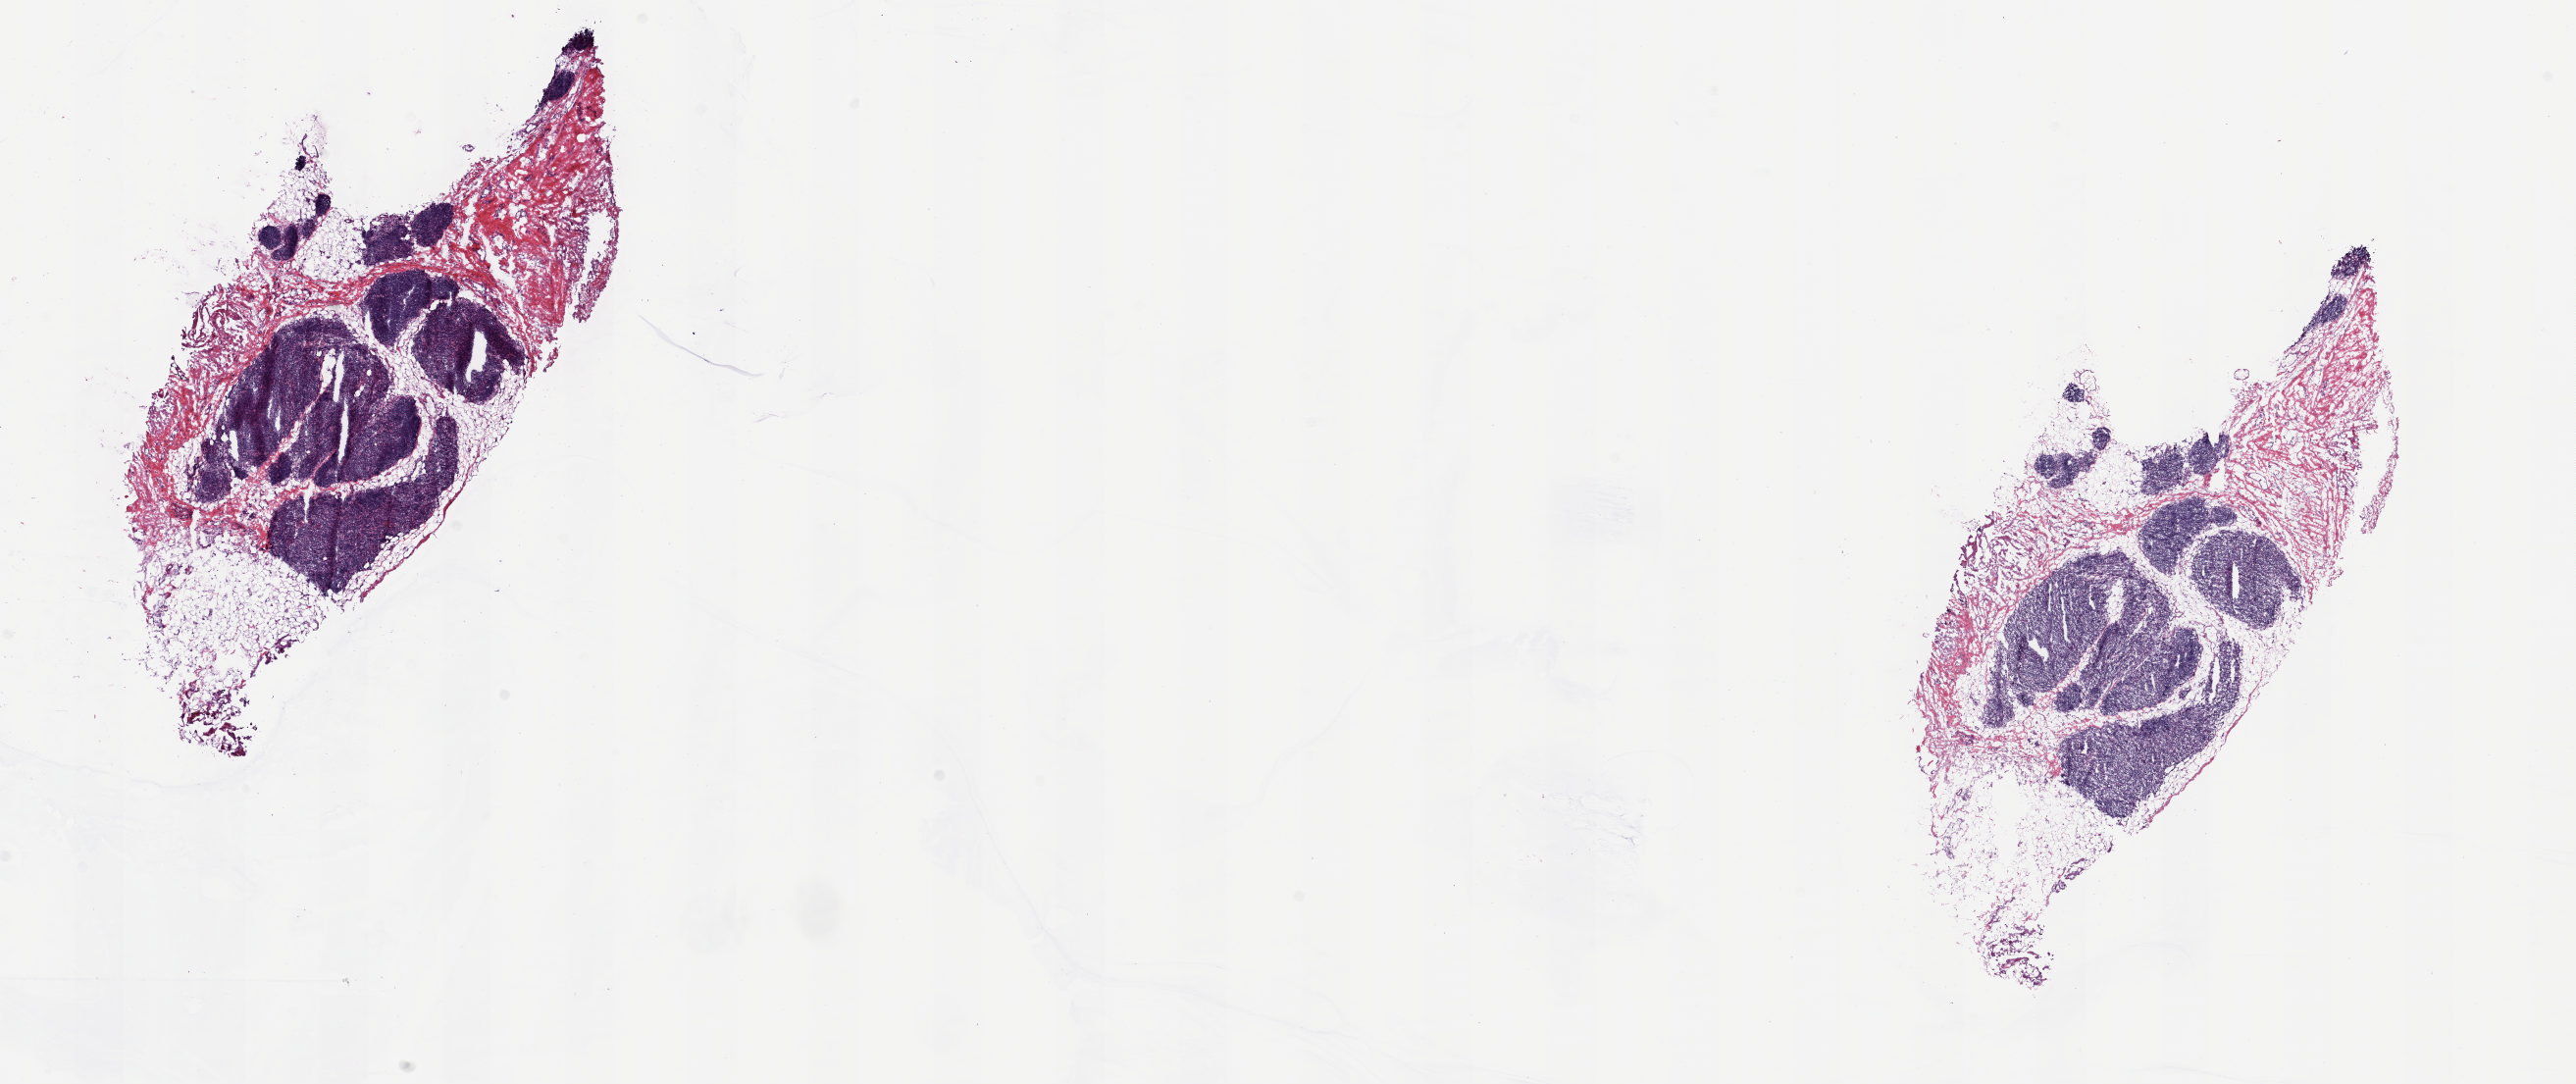
Digitized Hematoxylin and eosin (H&E) stained tissue section (whole slide) — a low-resolution overview of the entire scanned area, about 20.8 x 8.8 mm; frozen section; thymus, solid tissue normal (non-tumour tissue) sample. Patient: male, age at initial diagnosis 39 years. Composition of this section per pathologist review: tumour cells 0%, tumour nuclei 0%, normal cells 0%, stromal cells 100%, necrosis 0%. Inflammatory infiltration, as recorded: lymphocyte infiltration 80%, monocyte infiltration 1%, neutrophil infiltration 1%.
This section: solid tissue normal sample (biorepository sample class). Patient diagnosis: Thymoma, type AB, malignant.